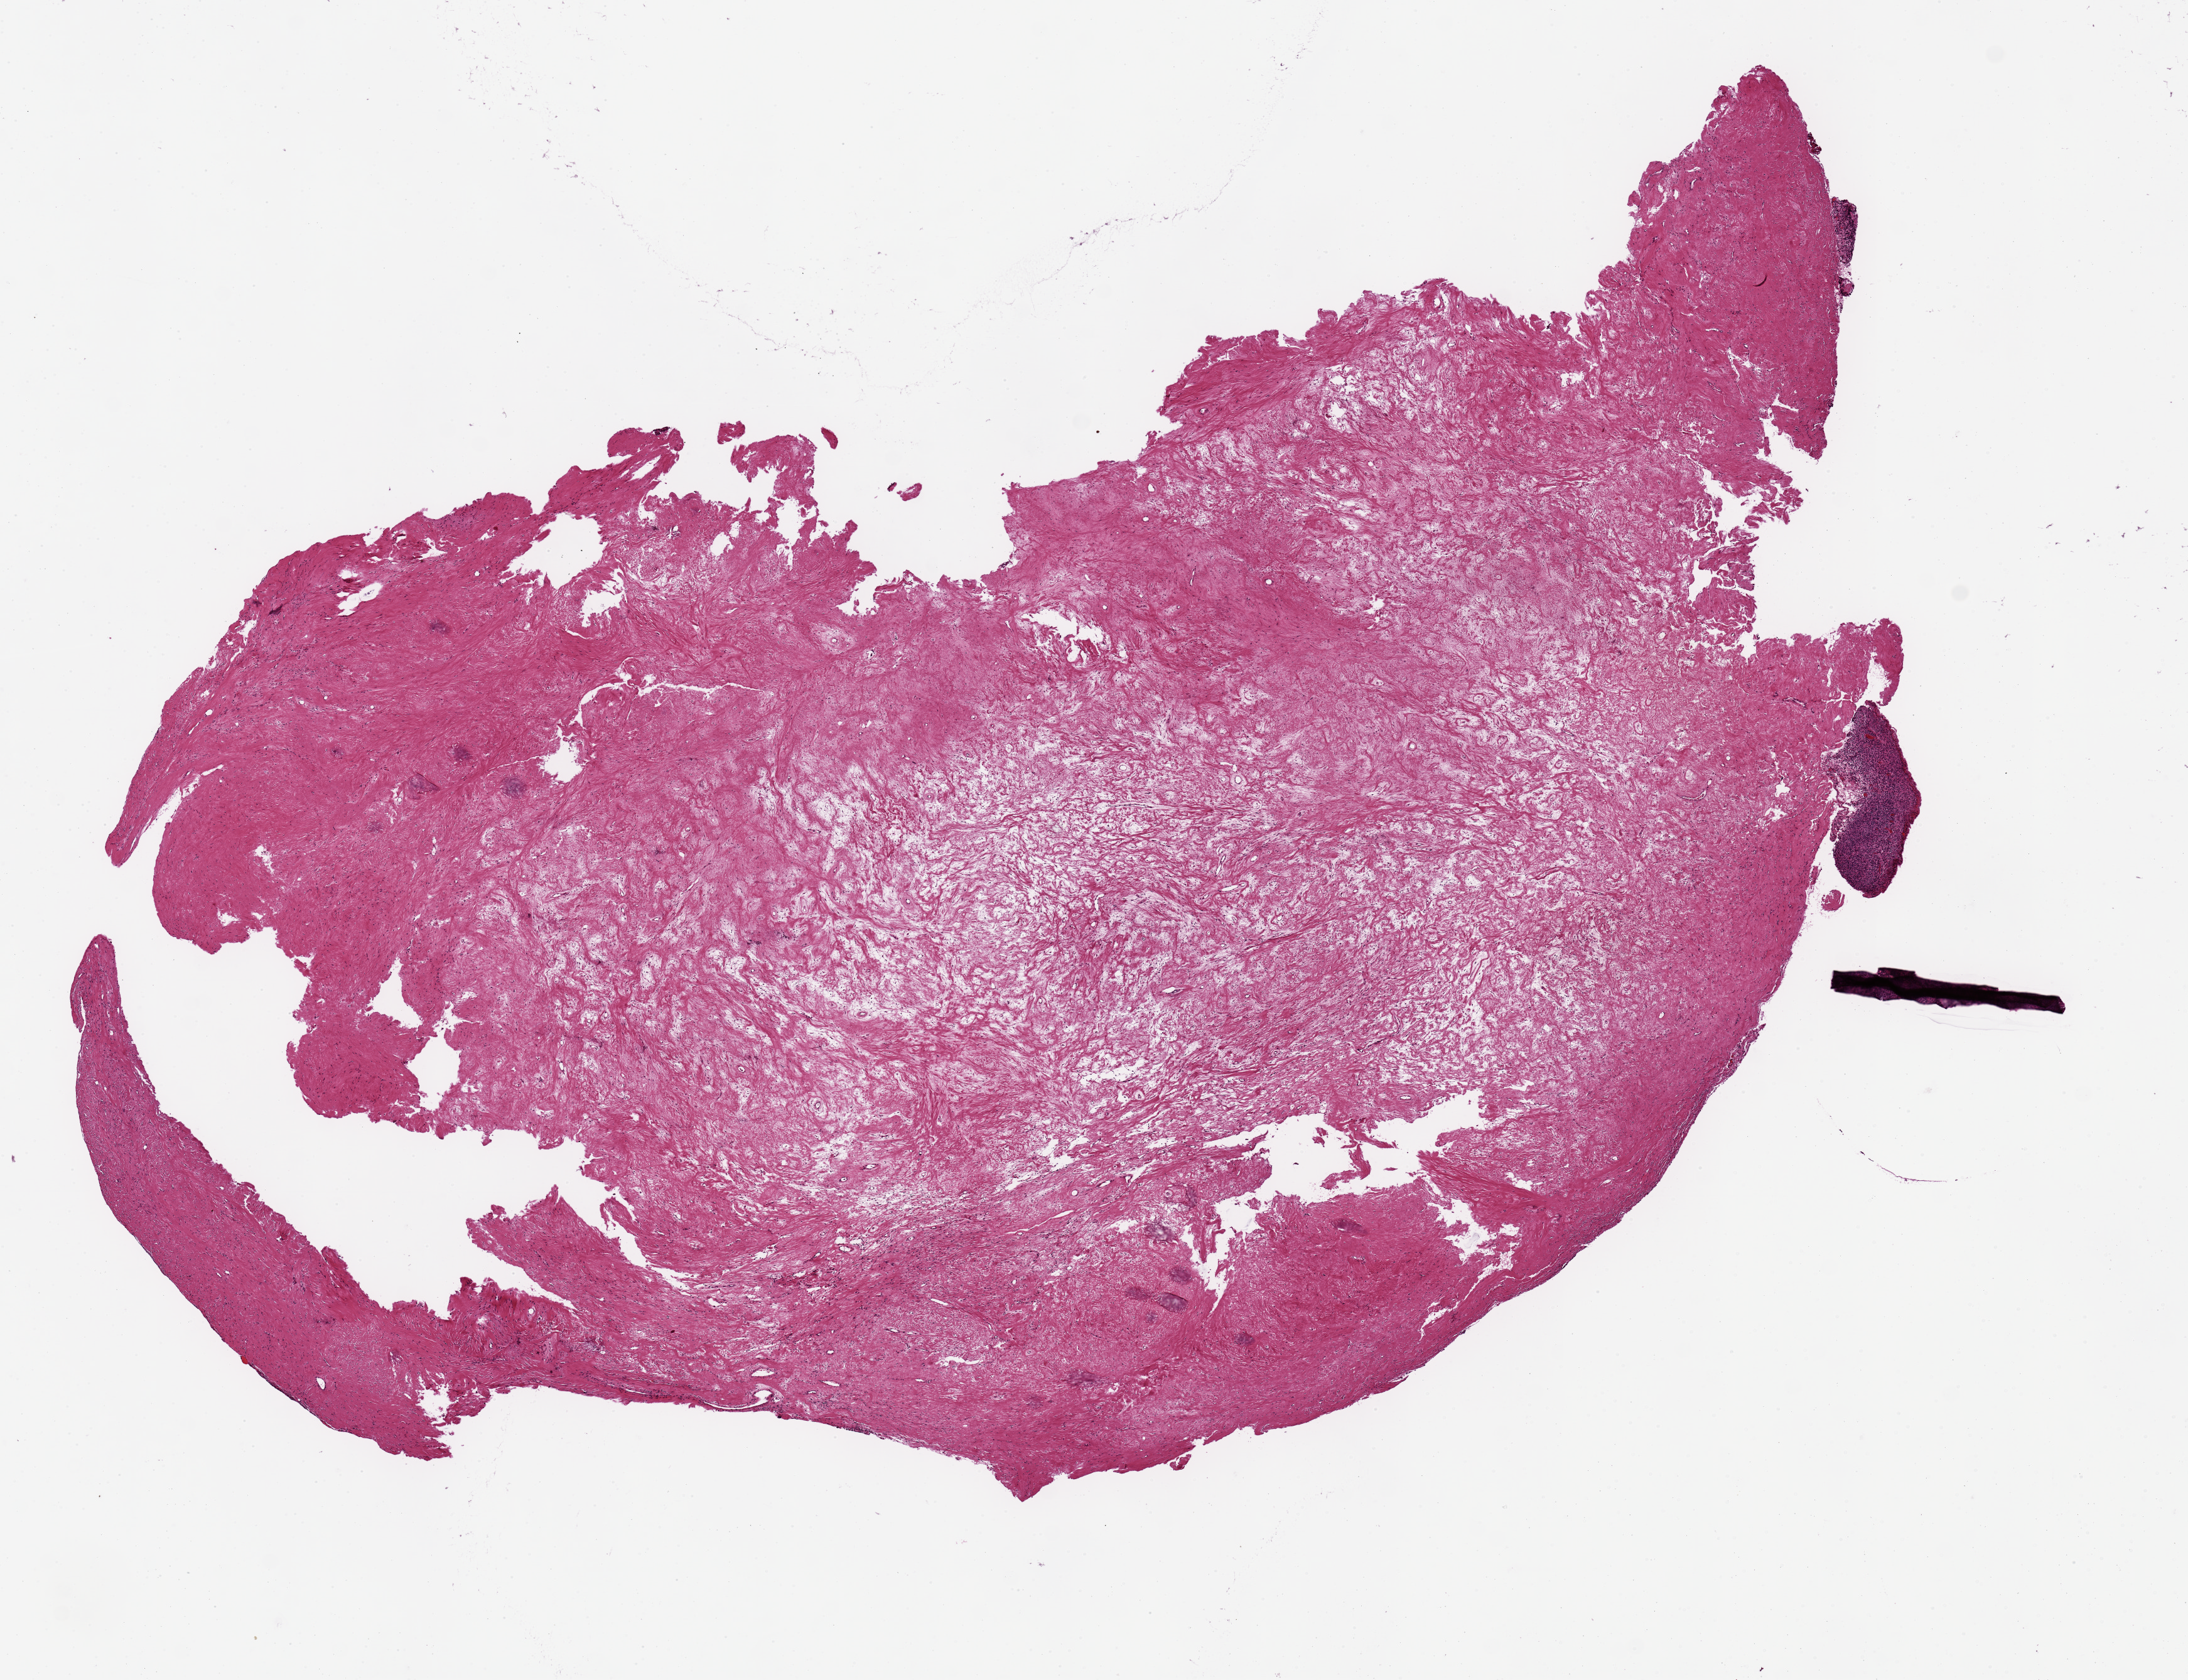
Whole-slide image, H&E stain, low-resolution overview of the scanned area, about 13.8 x 10.6 mm (acquisition: 20x scan), PAXgene-fixed, paraffin-embedded tissue, sampled site (target tissue): ovary, donor tissue sample.
* pathologist's review note for this sample: 2mm ovarian fragment with large fibroma (?) pending review of glass